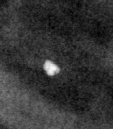
Cropped region of a digitized screen-film mammogram centred on a radiologist-marked abnormality; left breast; MLO view.
Marked abnormality: calcifications, morphology lucent centered; BI-RADS assessment category 2; benign; no additional work-up was recommended (benign without callback).